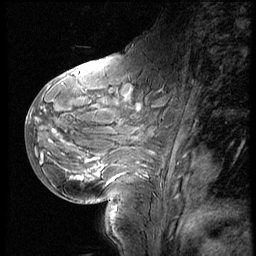
Breast MRI (dynamic contrast-enhanced), one sagittal slice; position 24 of 60 along the scan axis; 3 images stored at this slice position (order not interpretable as contrast timing); 1.5 T; TE 4.2 ms, TR 8.9 ms; 2.5 mm slice thickness; 256 × 256 image matrix, field of view 200 × 200 mm. Patient: female, 29 years. Case-level facts recorded for this patient, not image findings: setting: breast cancer imaged before/during neoadjuvant chemotherapy.
Annotated regions visible in this slice (semi-automatic segmentation, software-assisted and operator-edited):
- analysis volume of interest (the breast-tissue region the enhancement analysis was run in; not a lesion): bounding box <29,57,178,200> (left, top, right, bottom; pixels)
- tumour enhancement mask (voxels above the 140 % enhancement threshold inside the analysis volume of interest): <36,105,141,180>